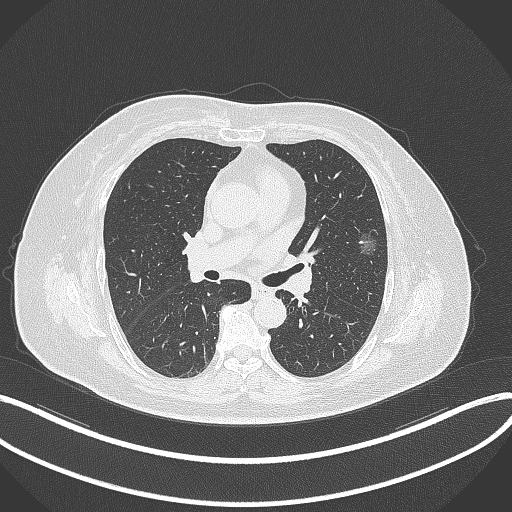
Chest CT, one axial slice. Position 204 of 315 along the scan axis. Reconstruction kernel B70f. Lung window (W 1500 / L -600 HU). 1 mm slice thickness. 512 × 512 image matrix, field of view 400 × 400 mm. Female patient, age 76 years. From the clinical record (not read from this slice): clinical TNM (as recorded): T1b N0 M0.
Annotated regions visible in this slice (rectangle marked by the reading radiologist):
- lung tumour (recorded histology: adenocarcinoma): bounding box (x1, y1, x2, y2) in pixels: (349, 222, 384, 261)